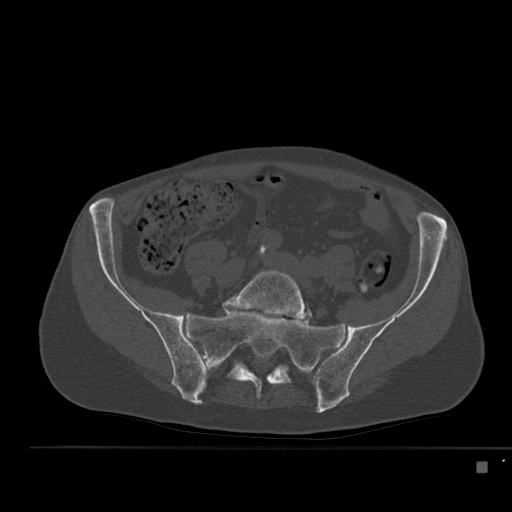
CT including the spine, one axial slice. Slice 111 of 517 in the series (ordered by position). Reconstruction kernel Br40s. 120 kVp. Bone window (W 1800 / L 400 HU). 1.5 mm slice thickness. 512 × 512 image matrix. Patient: male, 70 years. Case-level facts recorded for this patient, not image findings: primary cancer: renal; vertebrae with lytic lesions (as recorded): T4, T6, T10, T12, L3, L4, L5.
Annotated regions visible in this slice (semi-automatic segmentation, software-assisted and operator-edited):
- L5 vertebra: bounding box [x1, y1, x2, y2] px = [223, 269, 312, 321]